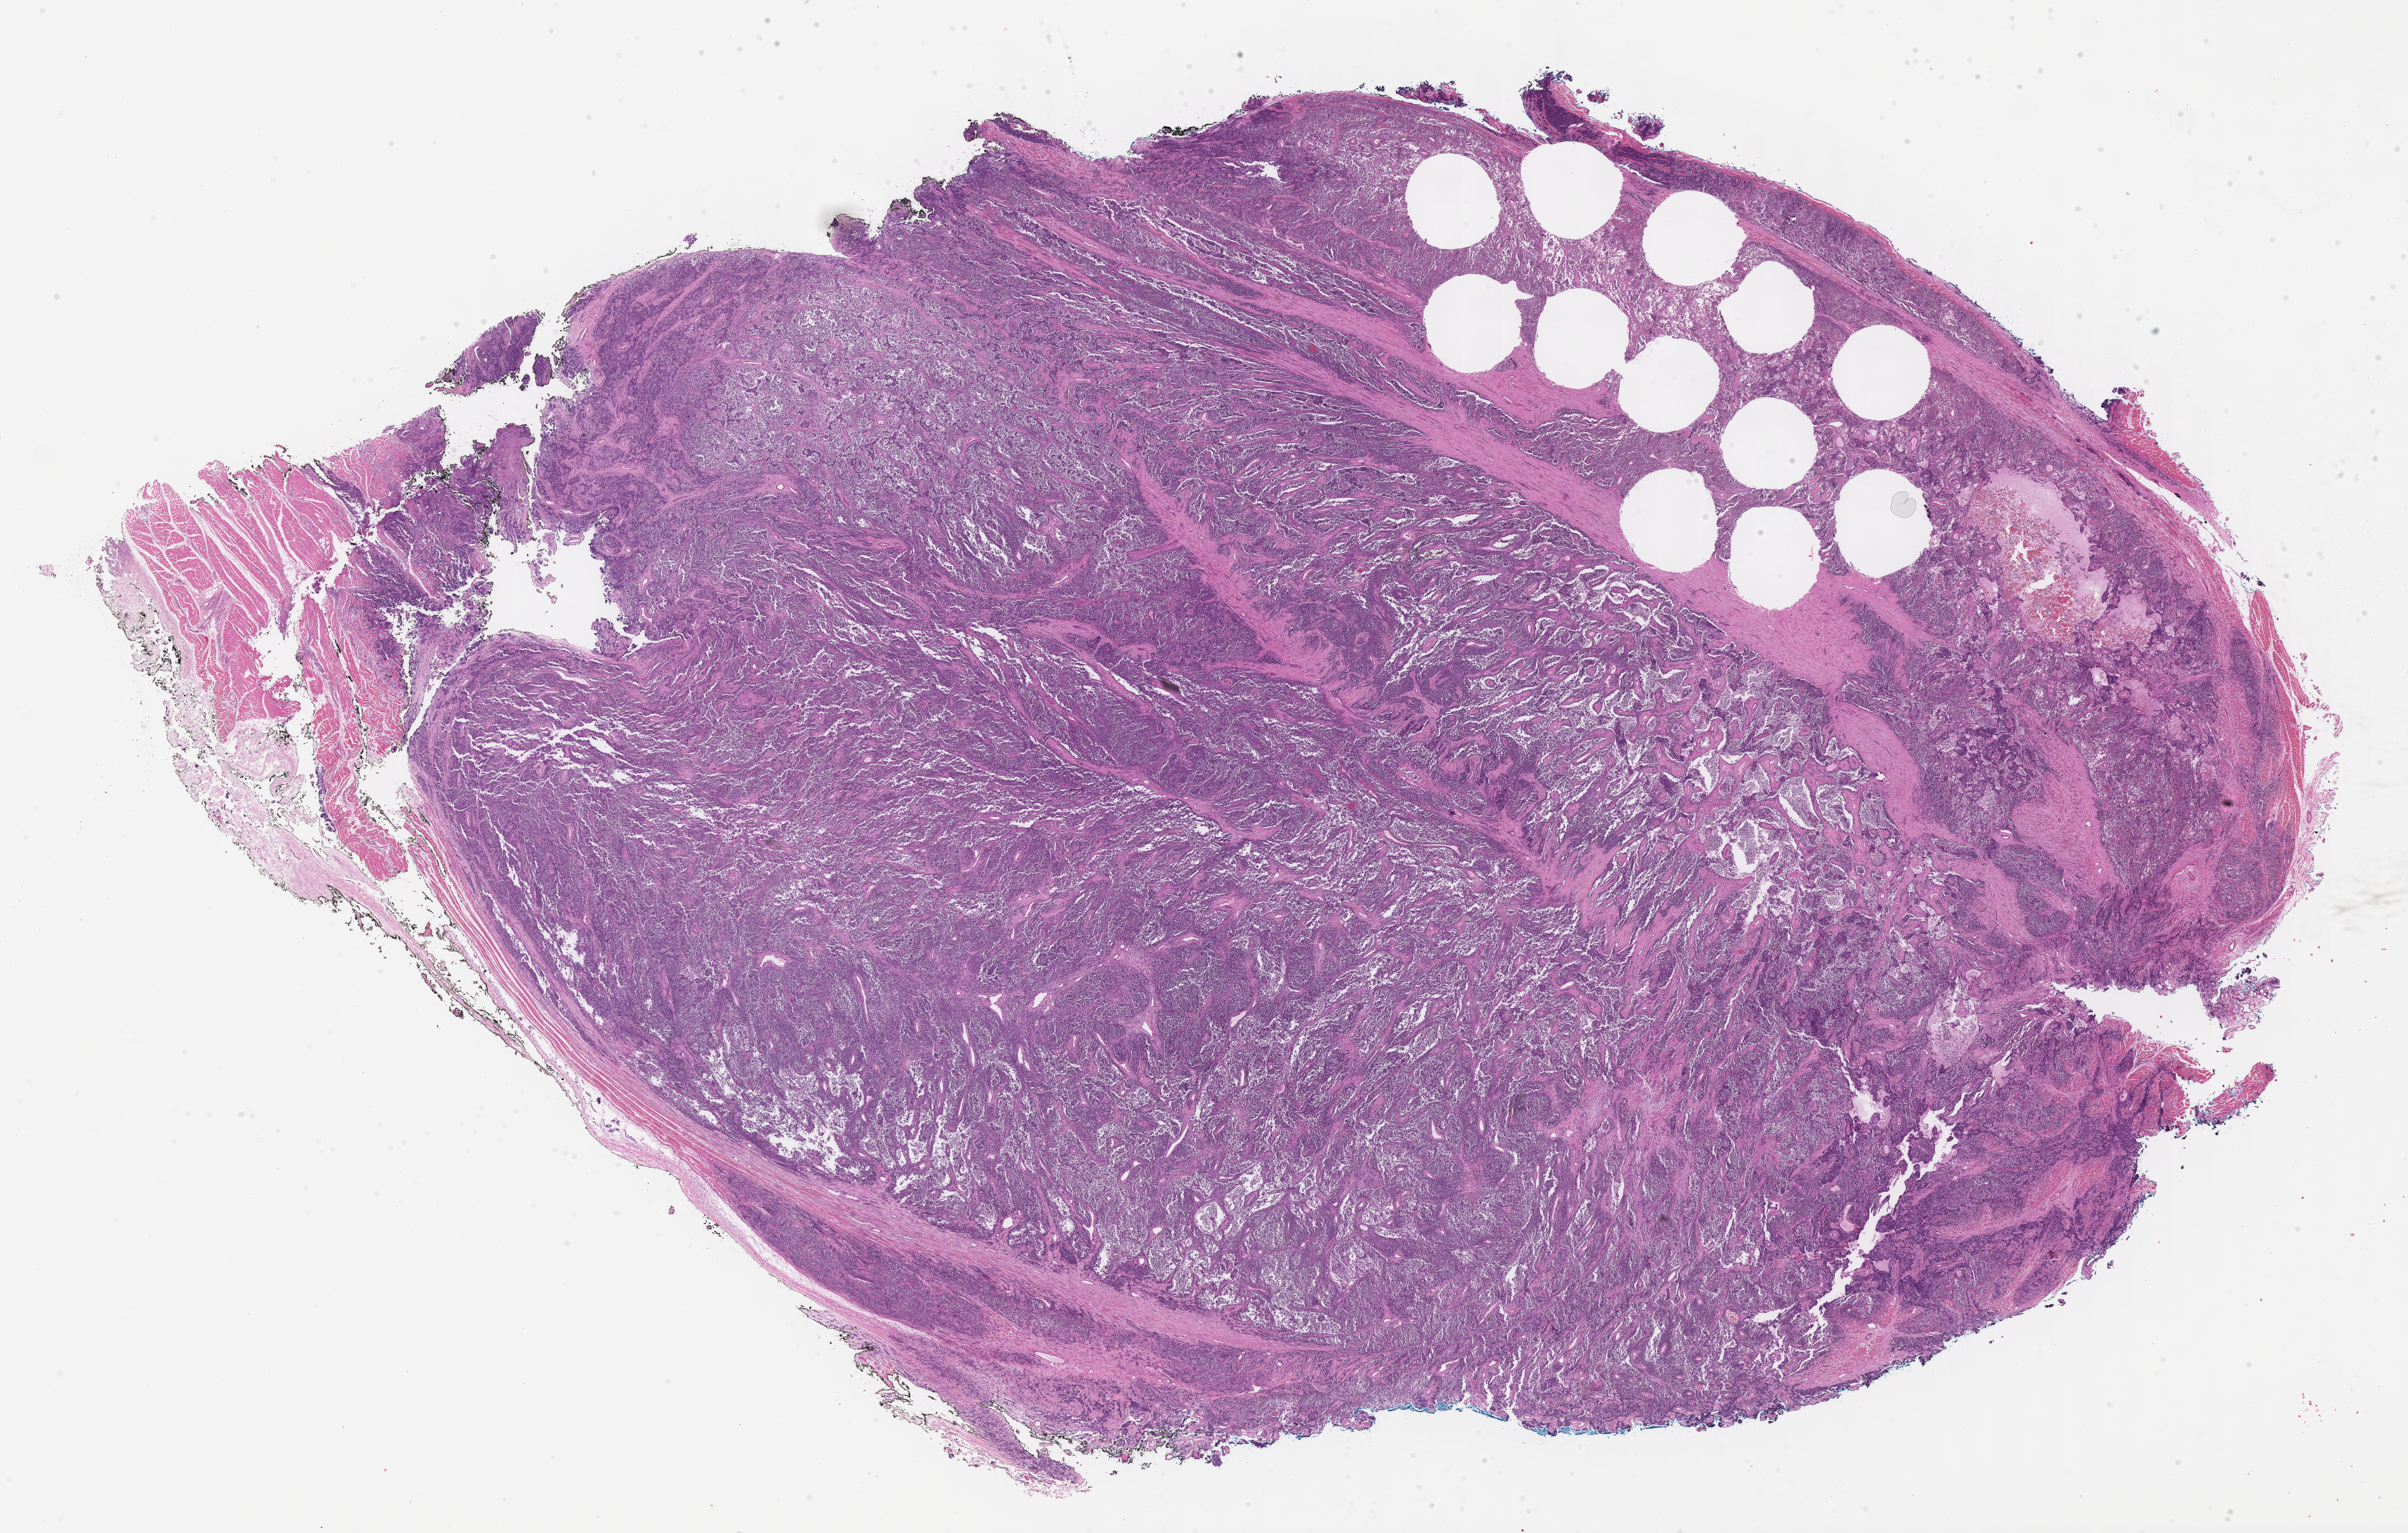
Whole-slide image, H&E stain of tumor tissue, low-resolution overview of the scanned area, about 30.7 x 19.5 mm. Formalin-fixed, paraffin-embedded (FFPE) tissue. Sample anatomic site: thigh, left. Male patient, age at diagnosis 1.8 years.
Metastatic status at presentation (as recorded): non-metastatic. Stage (as recorded): 2. Diagnosis: rhabdomyosarcoma; histological classification: alveolar rhabdomyosarcoma.